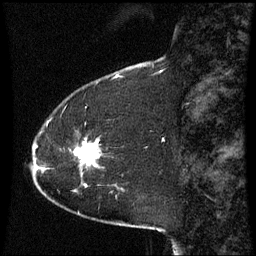
Breast MRI (dynamic contrast-enhanced), one sagittal slice. Slice 12 of 60 in the series (ordered by position). Dynamic contrast-enhanced series, image 2 of 3 at this slice position (ordered by acquisition). 1.5 T. TE 4.2 ms, TR 8.9 ms. 256 × 256 image matrix, field of view 210 × 210 mm. Female patient, age 51 years. Case-level facts recorded for this patient, not image findings: setting: breast cancer imaged before/during neoadjuvant chemotherapy; receptor status: HR-positive, HER2-negative.
Structures marked on this image (semi-automatic segmentation, software-assisted and operator-edited):
- analysis volume of interest (the breast-tissue region the enhancement analysis was run in; not a lesion): bounding box (x1, y1, x2, y2) in pixels: (75, 140, 101, 187)
- tumour enhancement mask (voxels above the 70 % enhancement threshold inside the analysis volume of interest): (76, 141, 99, 166)